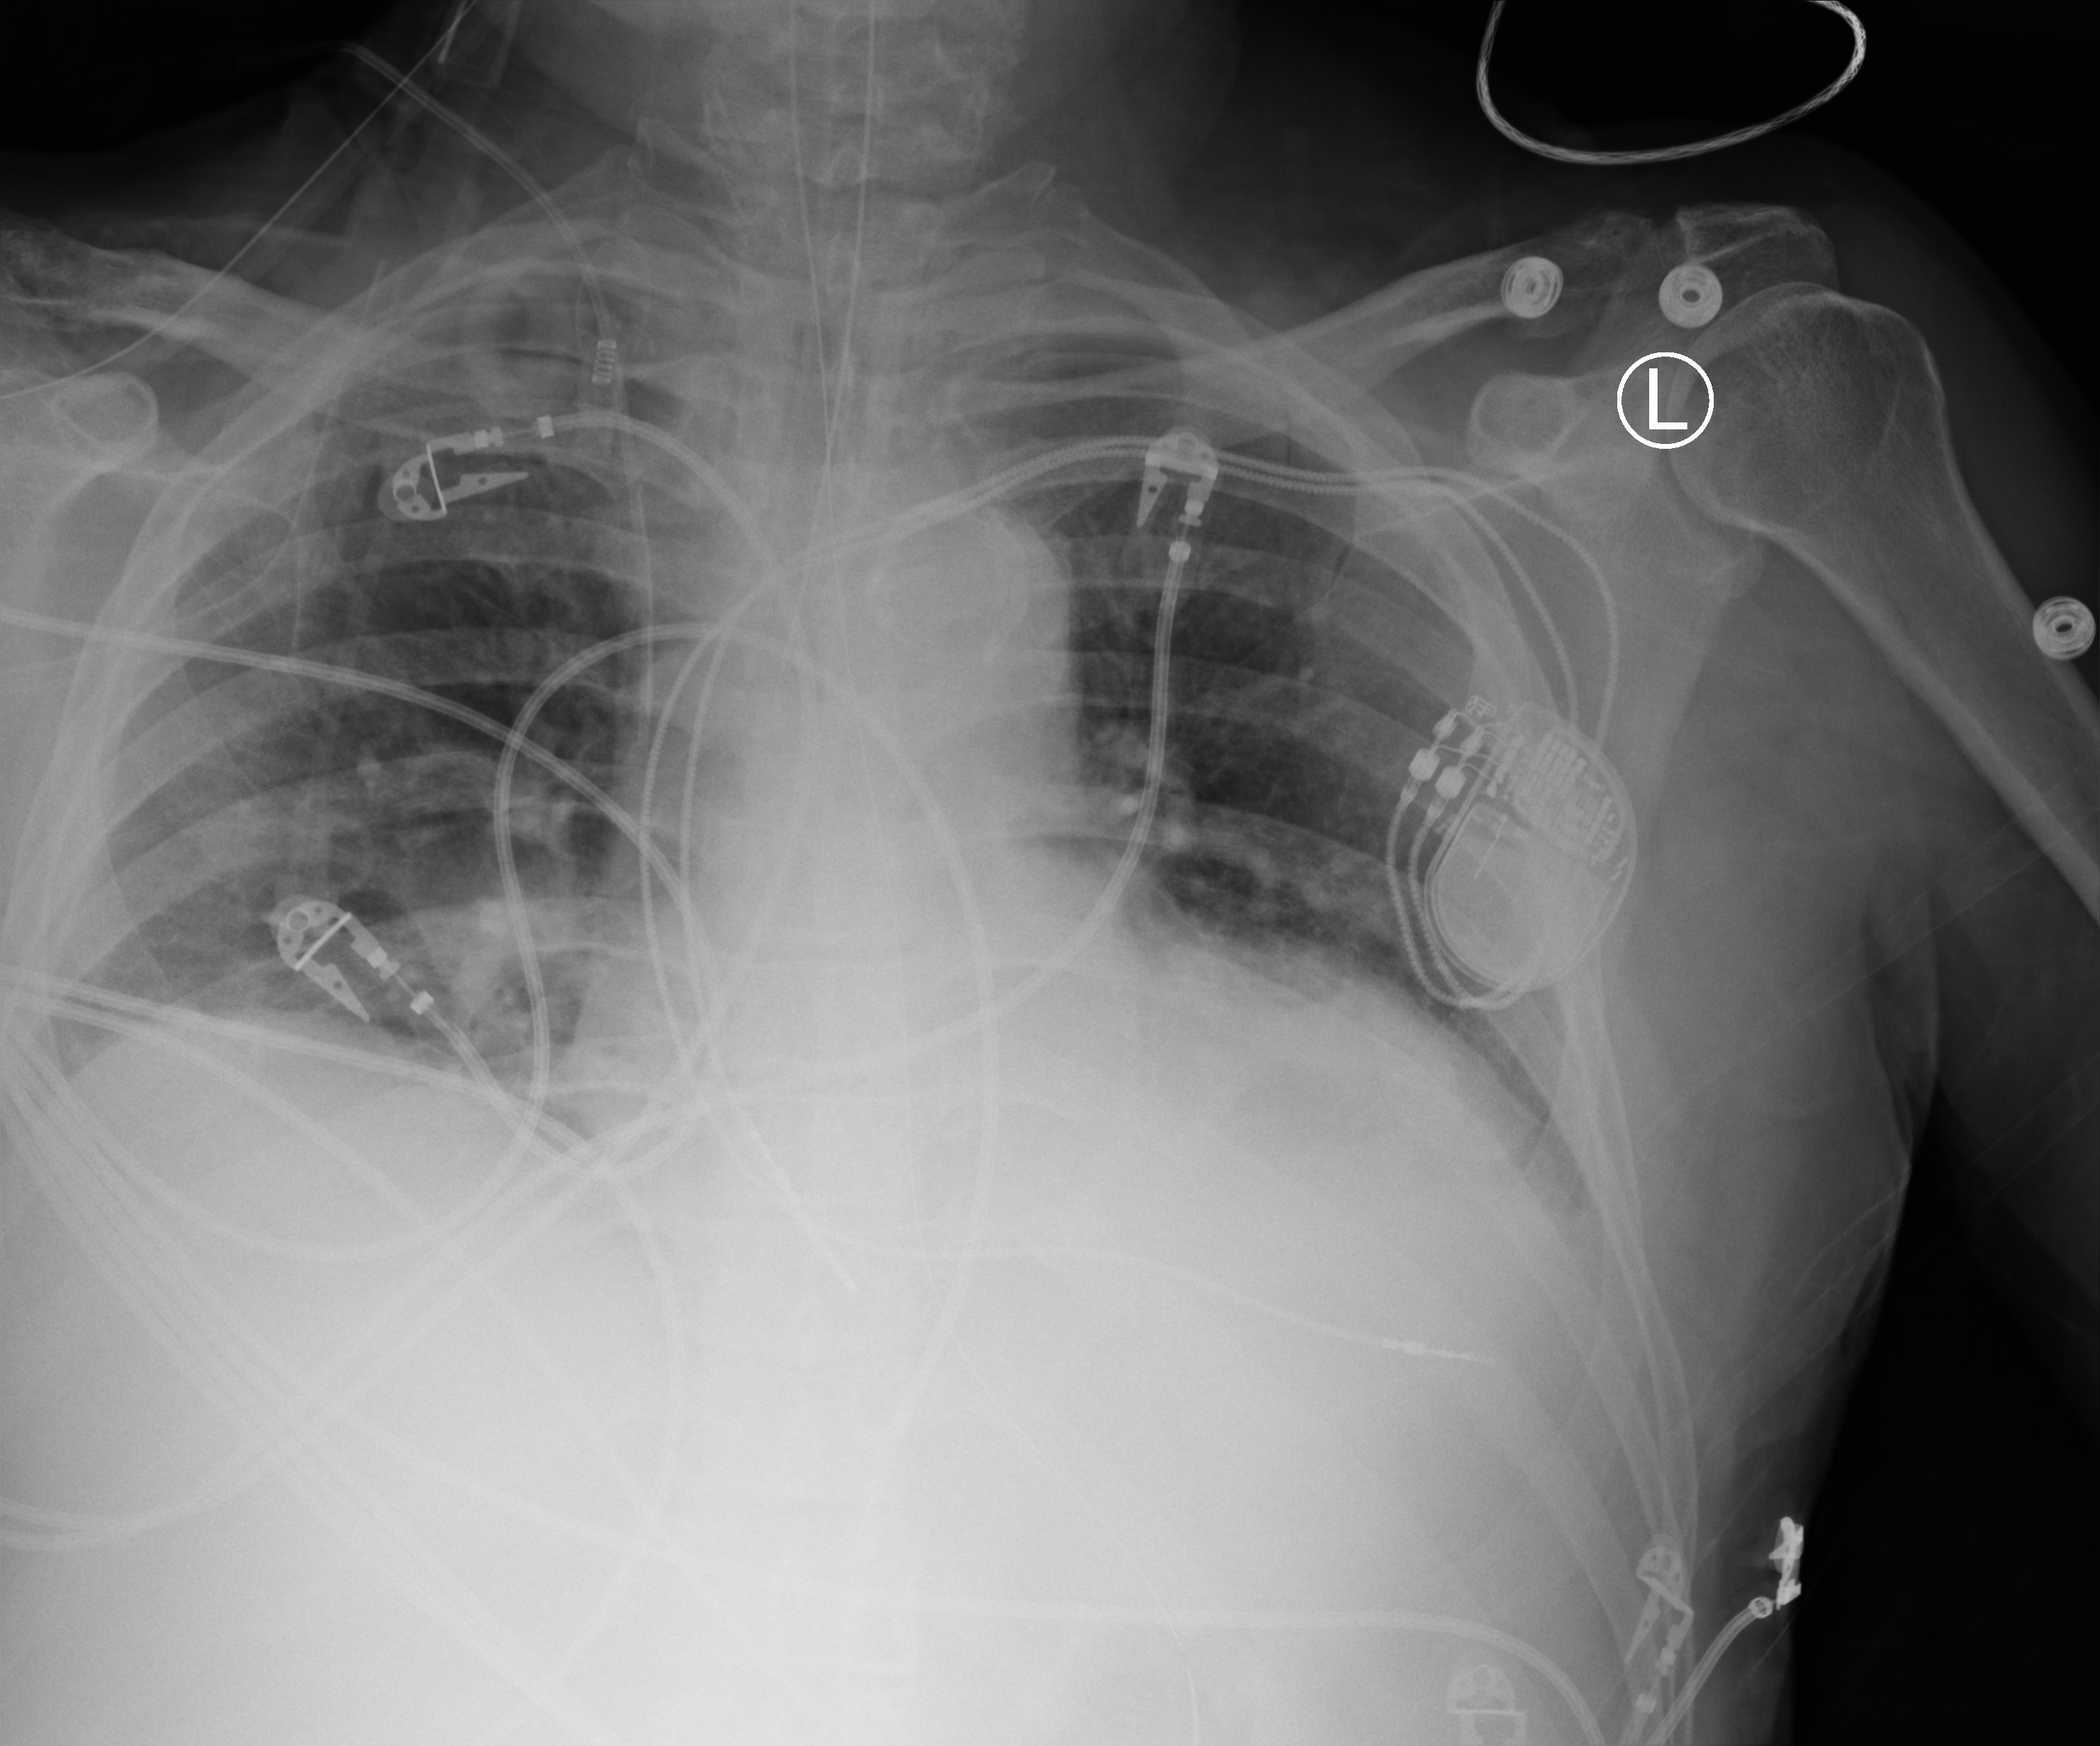
Chest X-ray (portable), anteroposterior (AP) projection. Patient hospitalised with COVID-19; male, aged 60–74 years.
Hospital-stay facts (about this admission, not read from this image; timing relative to this image not recorded): mechanically ventilated during this hospital stay: yes.